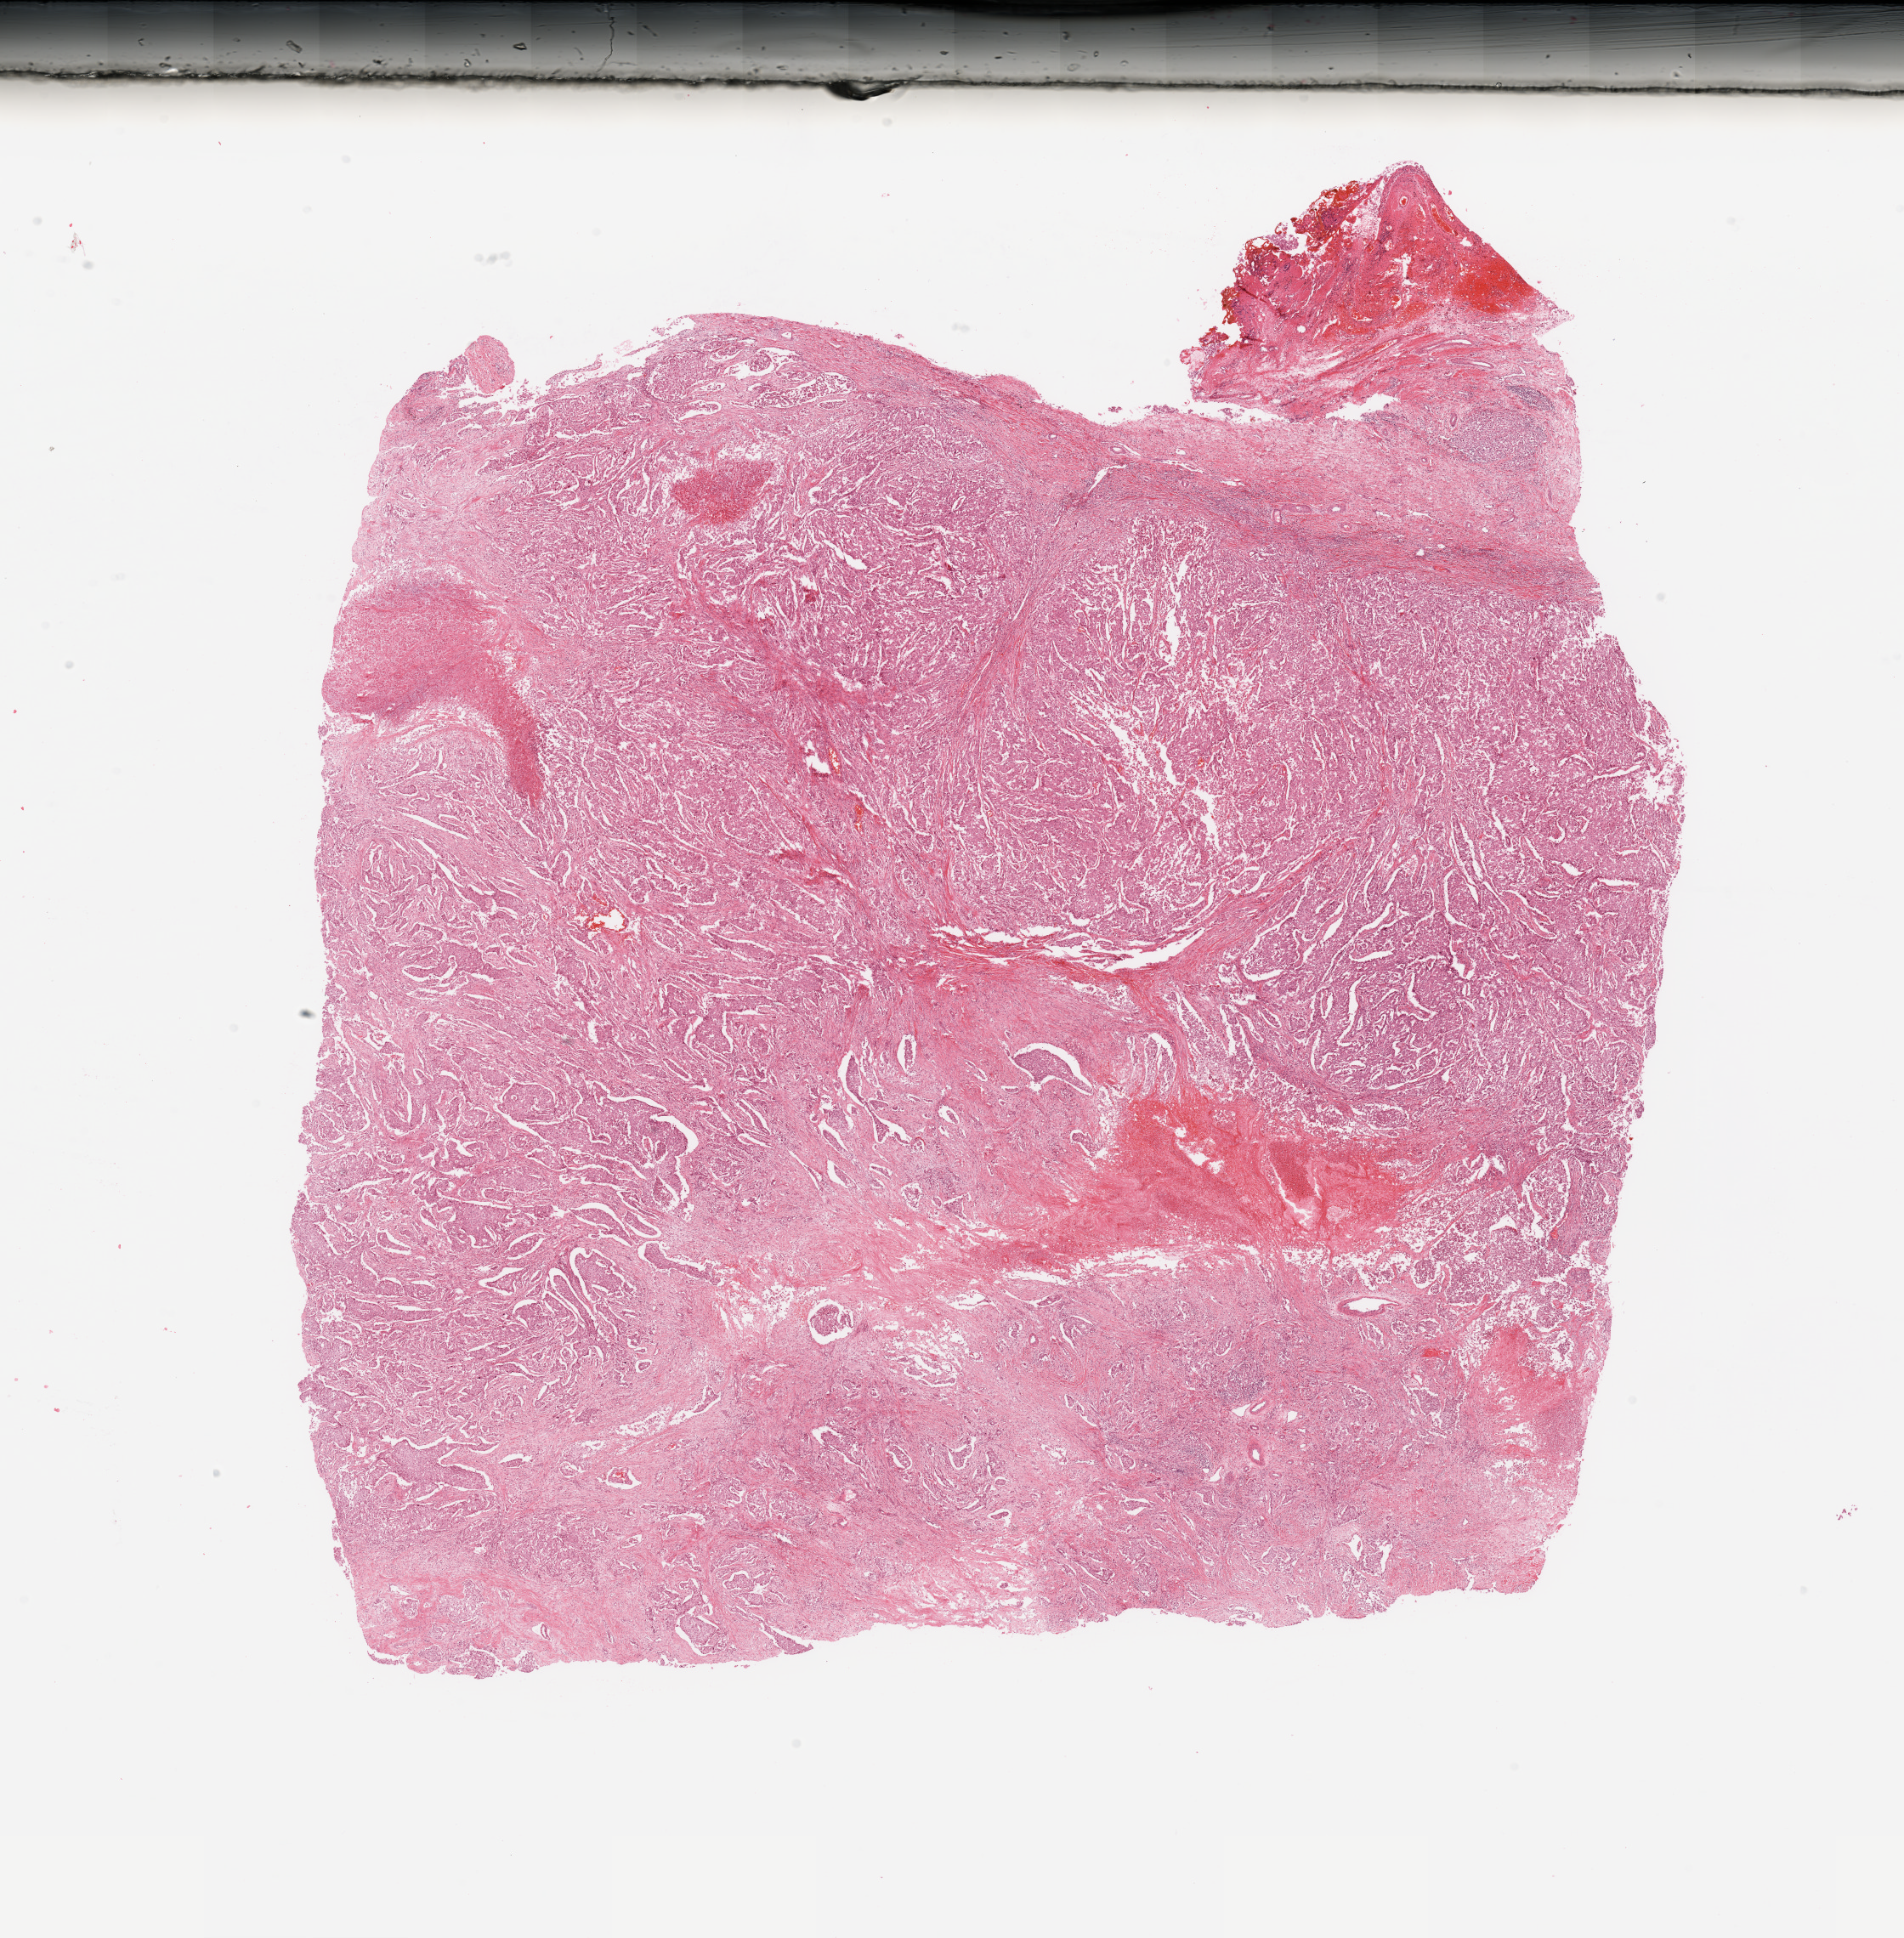
Digitized H&E-stained tissue section (whole slide) — low-resolution overview of the scanned area, about 17.7 x 18.0 mm (acquisition: 20x scan), lung, tumour tissue. Female, 49 y/o. Histologic grade: G3 (poorly differentiated).
• AJCC pathologic stage: IB
• histologic diagnosis: Adenocarcinoma, NOS